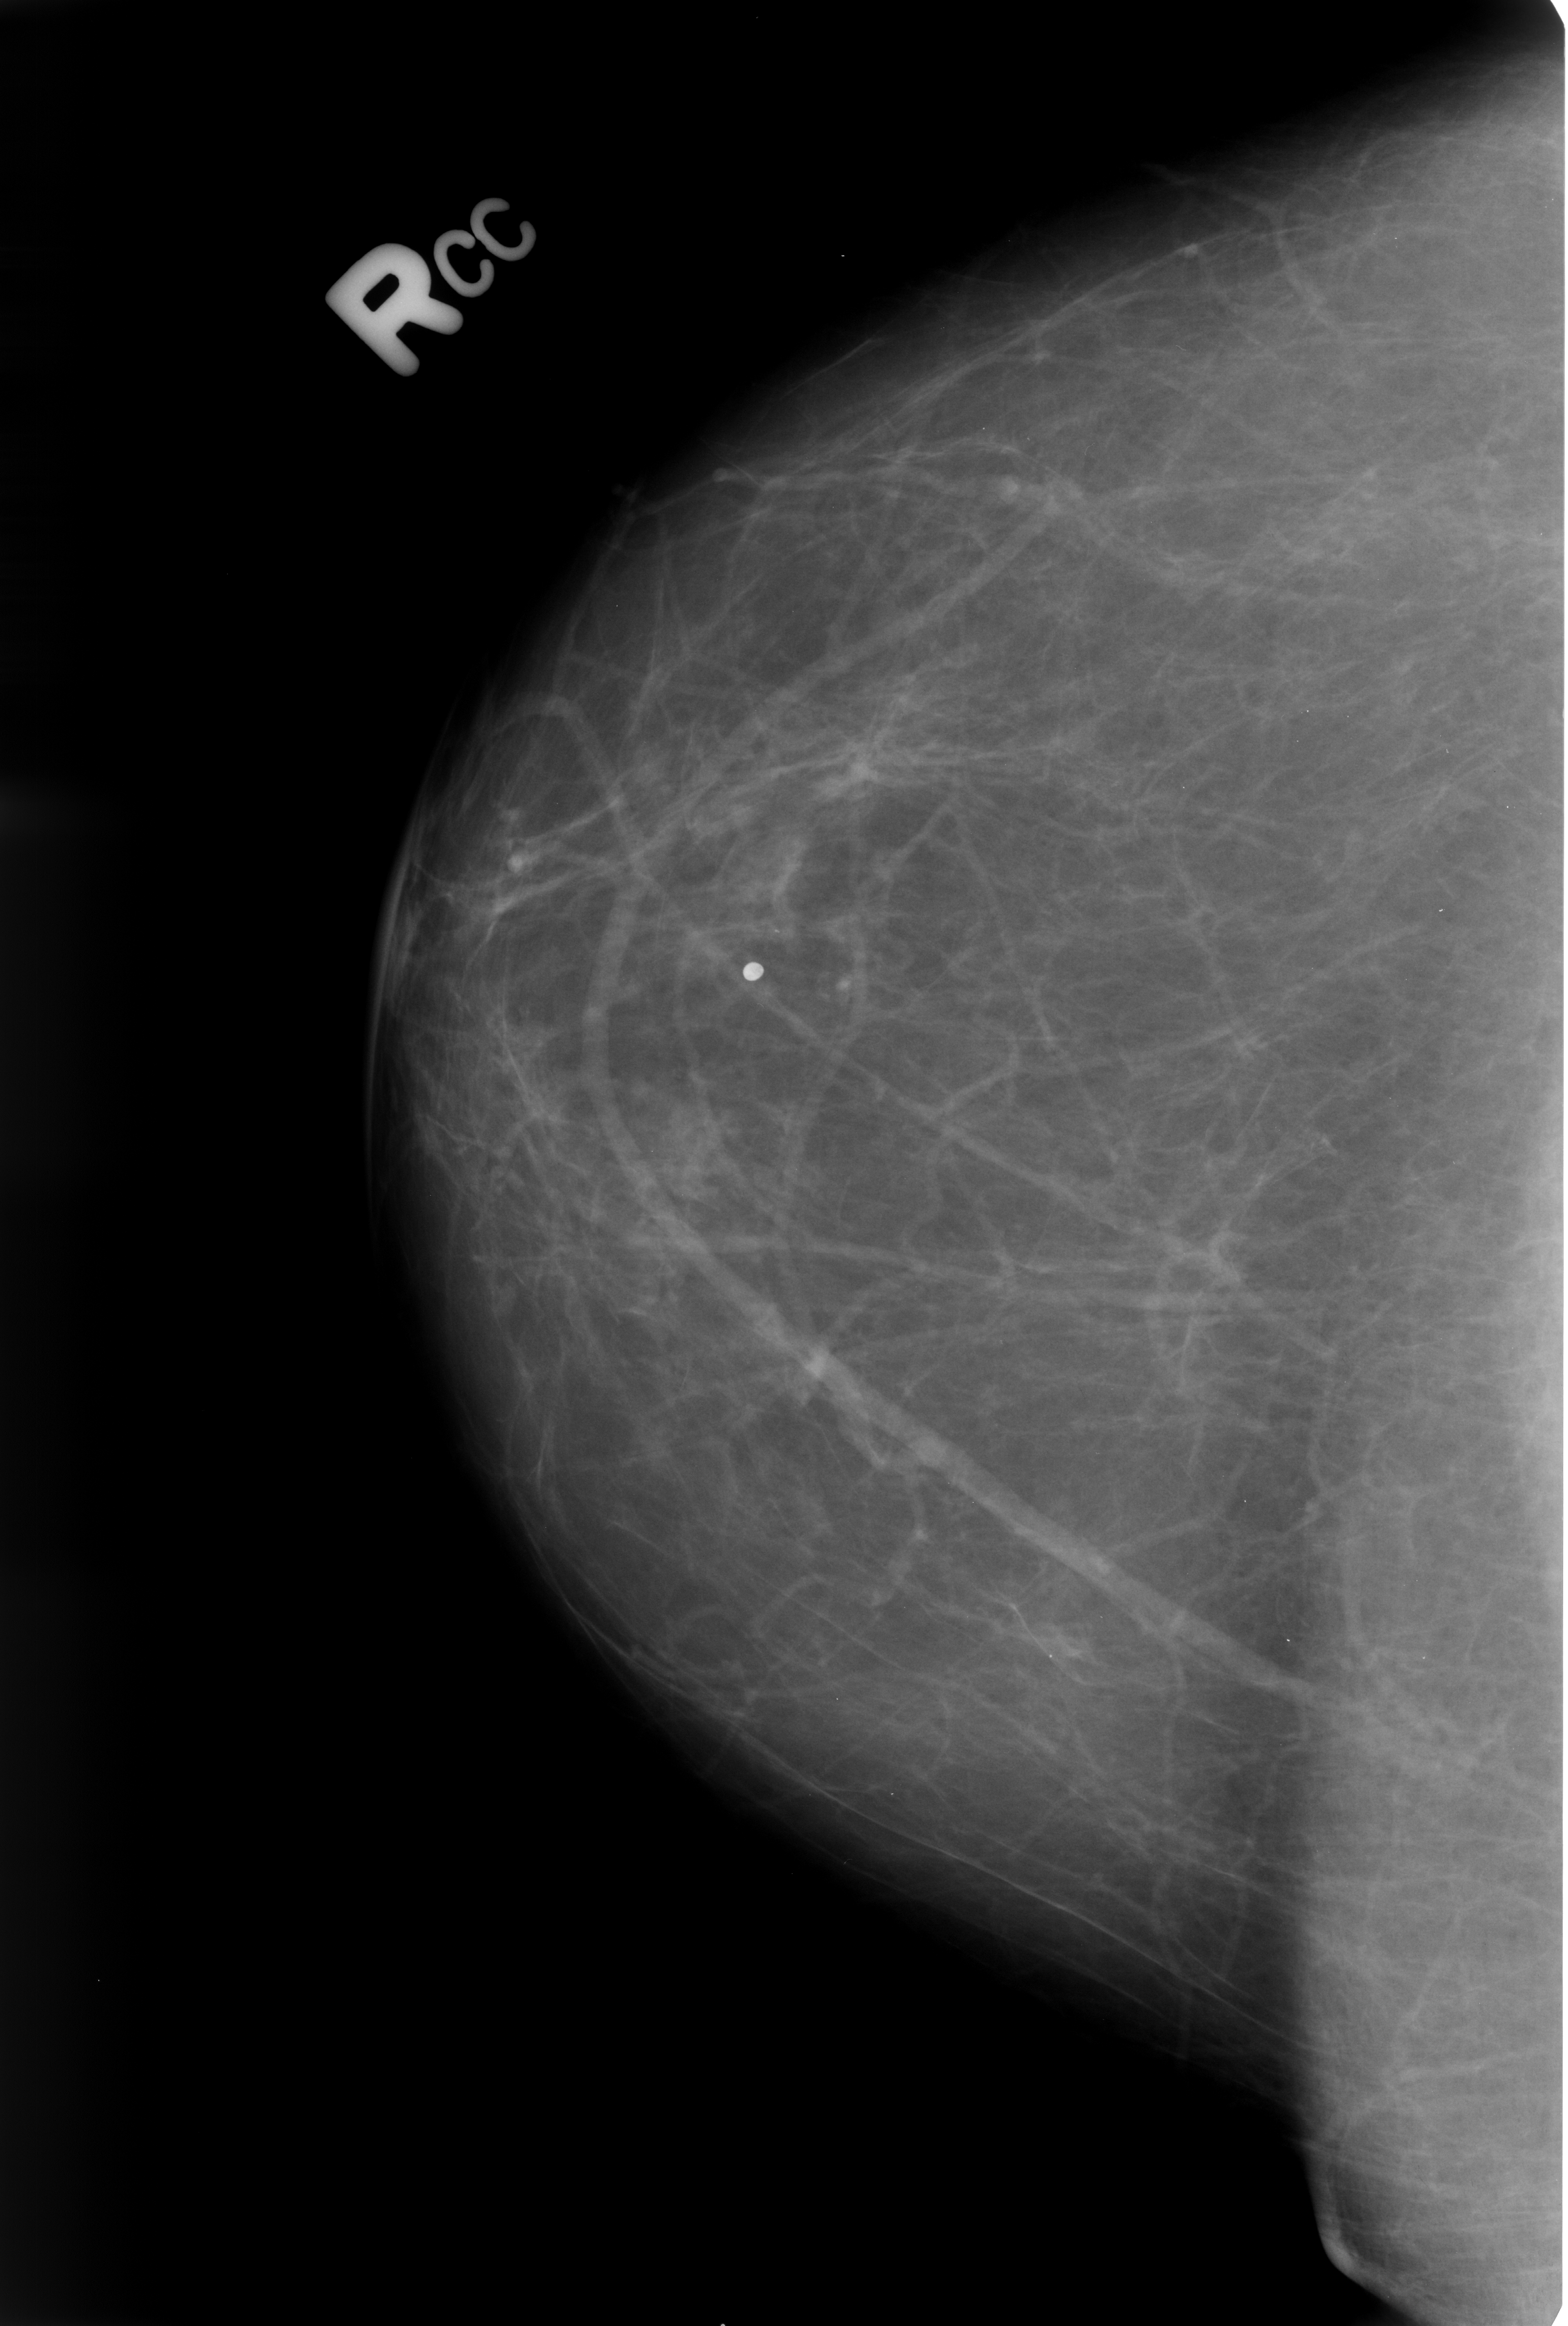
Mammogram (digitized film). Right breast. CC view. BI-RADS breast density category 2 (scale 1–4). 1568 × 2326 image matrix.
Marked abnormalities (boxes around the expert regions of interest):
- calcifications, morphology lucent center; BI-RADS assessment category 2; benign; no additional work-up was recommended (outcome (as recorded, no biopsy): benign without callback): bounding box <696,920,807,1023> (left, top, right, bottom; pixels)